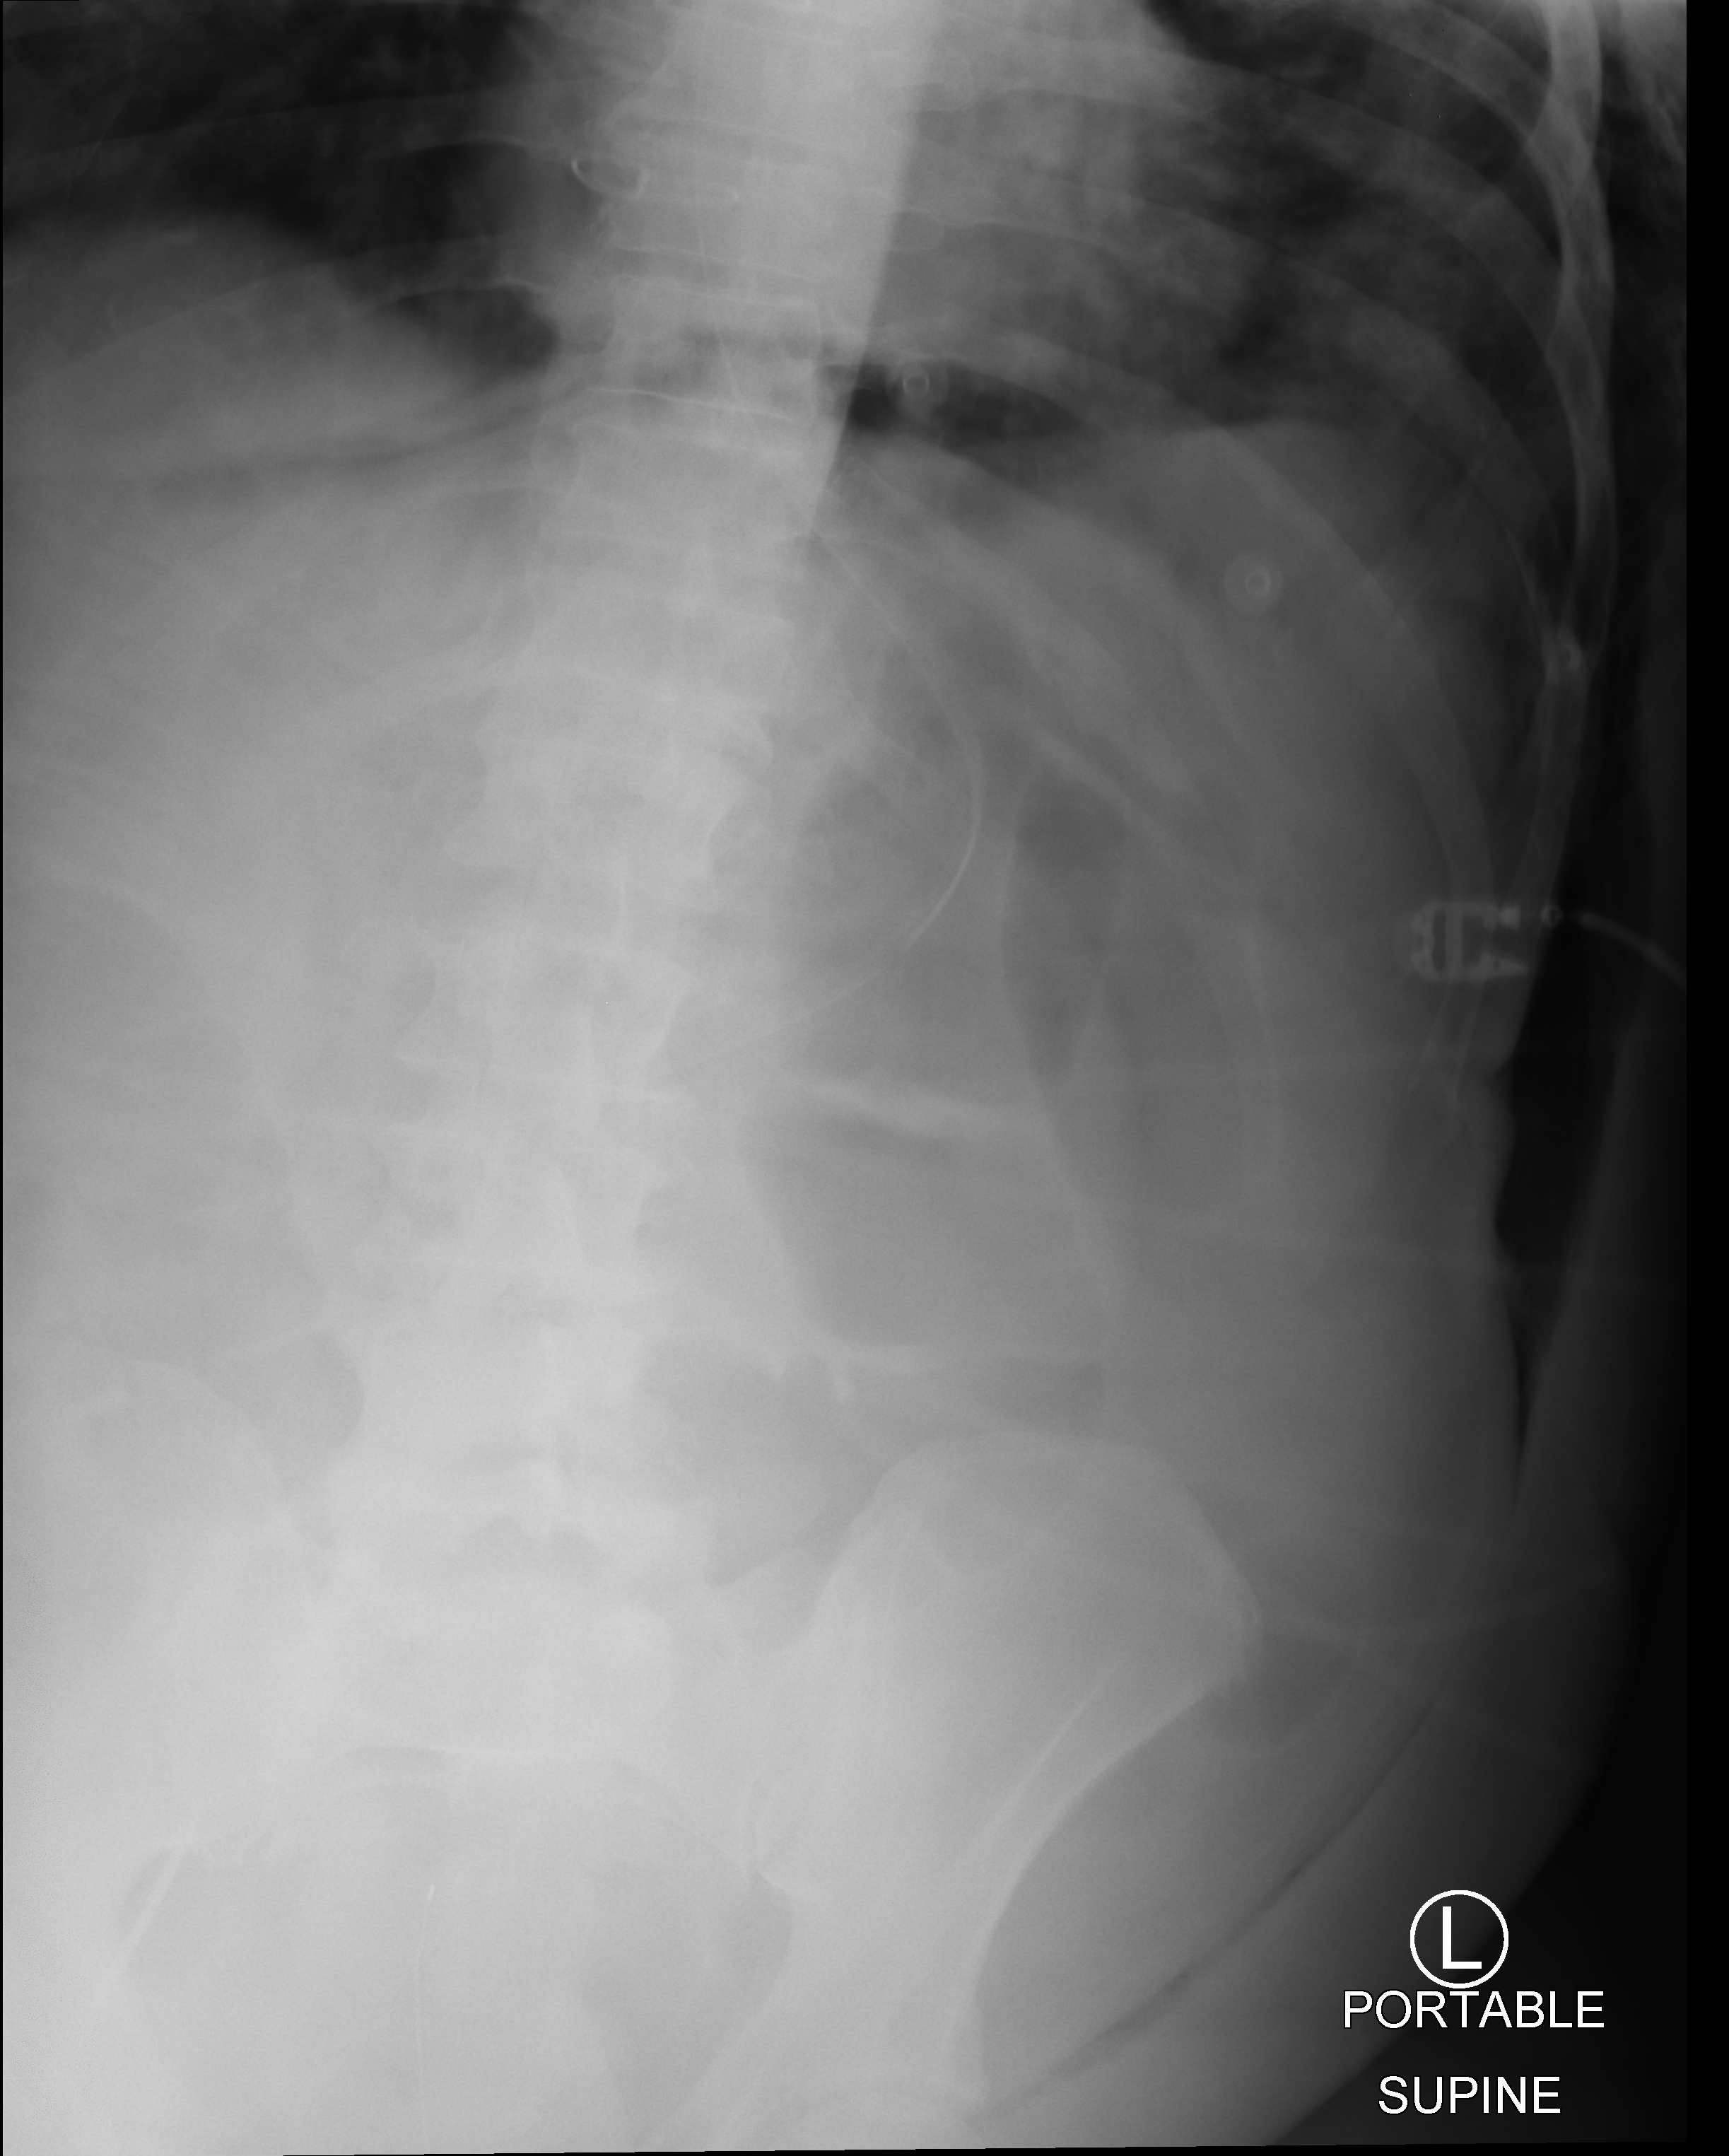
Bedside abdomen radiograph (computed radiography). Patient hospitalised with COVID-19; male, aged 60–74 years.
Admission-level facts for this patient (not findings on this image; timing relative to this image not recorded): diabetes (admission record): yes.